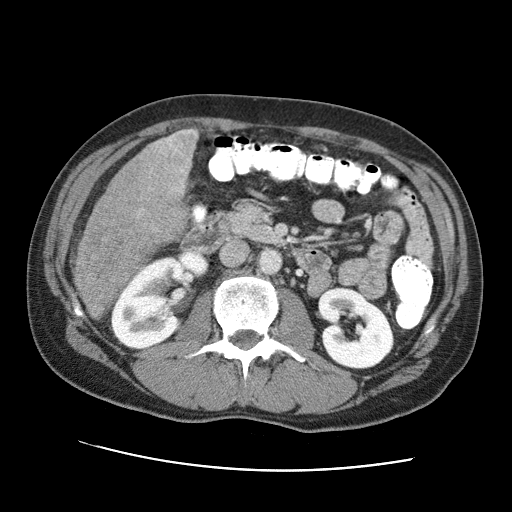
Contrast-enhanced abdominal CT (liver protocol), one axial slice. Slice 23 of 95 in the series (ordered by position). Reconstruction kernel STANDARD. 120 kVp. One of 2 acquisitions stored at this slice position. Soft-tissue window (W 400 / L 40 HU). 2.5 mm slice thickness. 512 × 512 image matrix, field of view 360 × 360 mm. From the clinical record (not read from this slice): diagnosis: hepatocellular carcinoma (patient treated with transarterial chemoembolisation; whether this scan precedes or follows treatment is not stated here); TNM stage (as recorded): Stage-IVA; Child-Pugh class: A.
Annotated regions visible in this slice (semi-automatic segmentation, software-assisted and operator-edited):
- liver parenchyma outside the tumour (the mass and vessels are separate outlines, so this box may not span the whole liver): bounding box <78,128,198,303> (left, top, right, bottom; pixels)
- mass: <73,128,197,322>